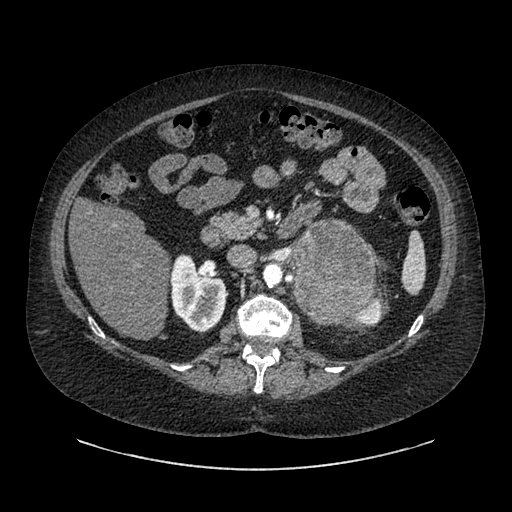
Contrast-enhanced abdominal CT, one axial slice. Slice 532 of 769 in the series (ordered by position). Intravenous contrast given. Soft-tissue window (W 400 / L 40 HU). 512 × 512 image matrix, field of view 460 × 460 mm. Female patient, age 61 years. Case-level facts recorded for this patient, not image findings: diagnosis: adrenocortical carcinoma; tumour side: left adrenal; tumour size at pathology: 13 cm; Ki-67 index: 79 %; stage (as recorded): 2.
Structures marked on this image (semi-automatically segmented with operator editing):
- mass: box from (x=295, y=222) to (x=373, y=323) px